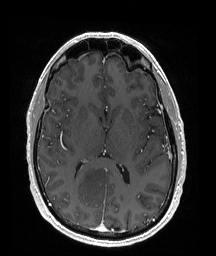
Brain MRI from a brain-tumour surgery series, one axial slice. Position 90 of 176 along the scan axis. T1-weighted post-contrast. 1 mm slice thickness. 216 × 256 image matrix, field of view 211 × 250 mm. From the clinical record (not read from this slice): histopathology: Oligodendroglioma; WHO grade: 2.
Annotated regions visible in this slice (expert manual segmentation):
- tumour: bounding box [x1, y1, x2, y2] px = [70, 164, 111, 202]